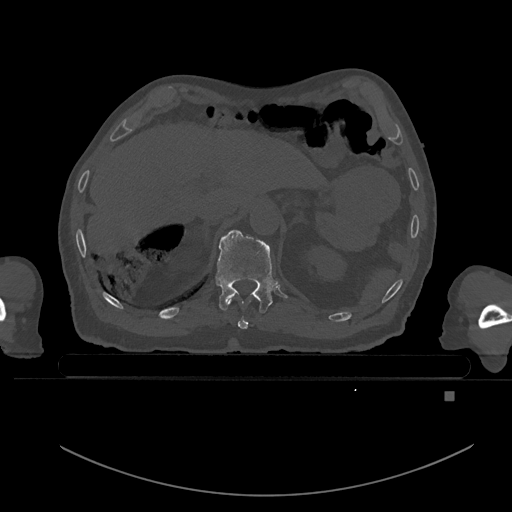
CT including the spine, one axial slice; slice 45 of 969 in the series (ordered by position); bone window (W 1800 / L 400 HU); 0.5 mm slice thickness; 512 × 512 image matrix, field of view 456 × 456 mm. Male patient, age 82 years. From the clinical record (not read from this slice): primary cancer: prostate.
Structures marked on this image (semi-automatic segmentation, software-assisted and operator-edited):
- T10 vertebra: bounding box (x1, y1, x2, y2) in pixels: (228, 300, 251, 330)
- T11 vertebra: (216, 229, 278, 313)